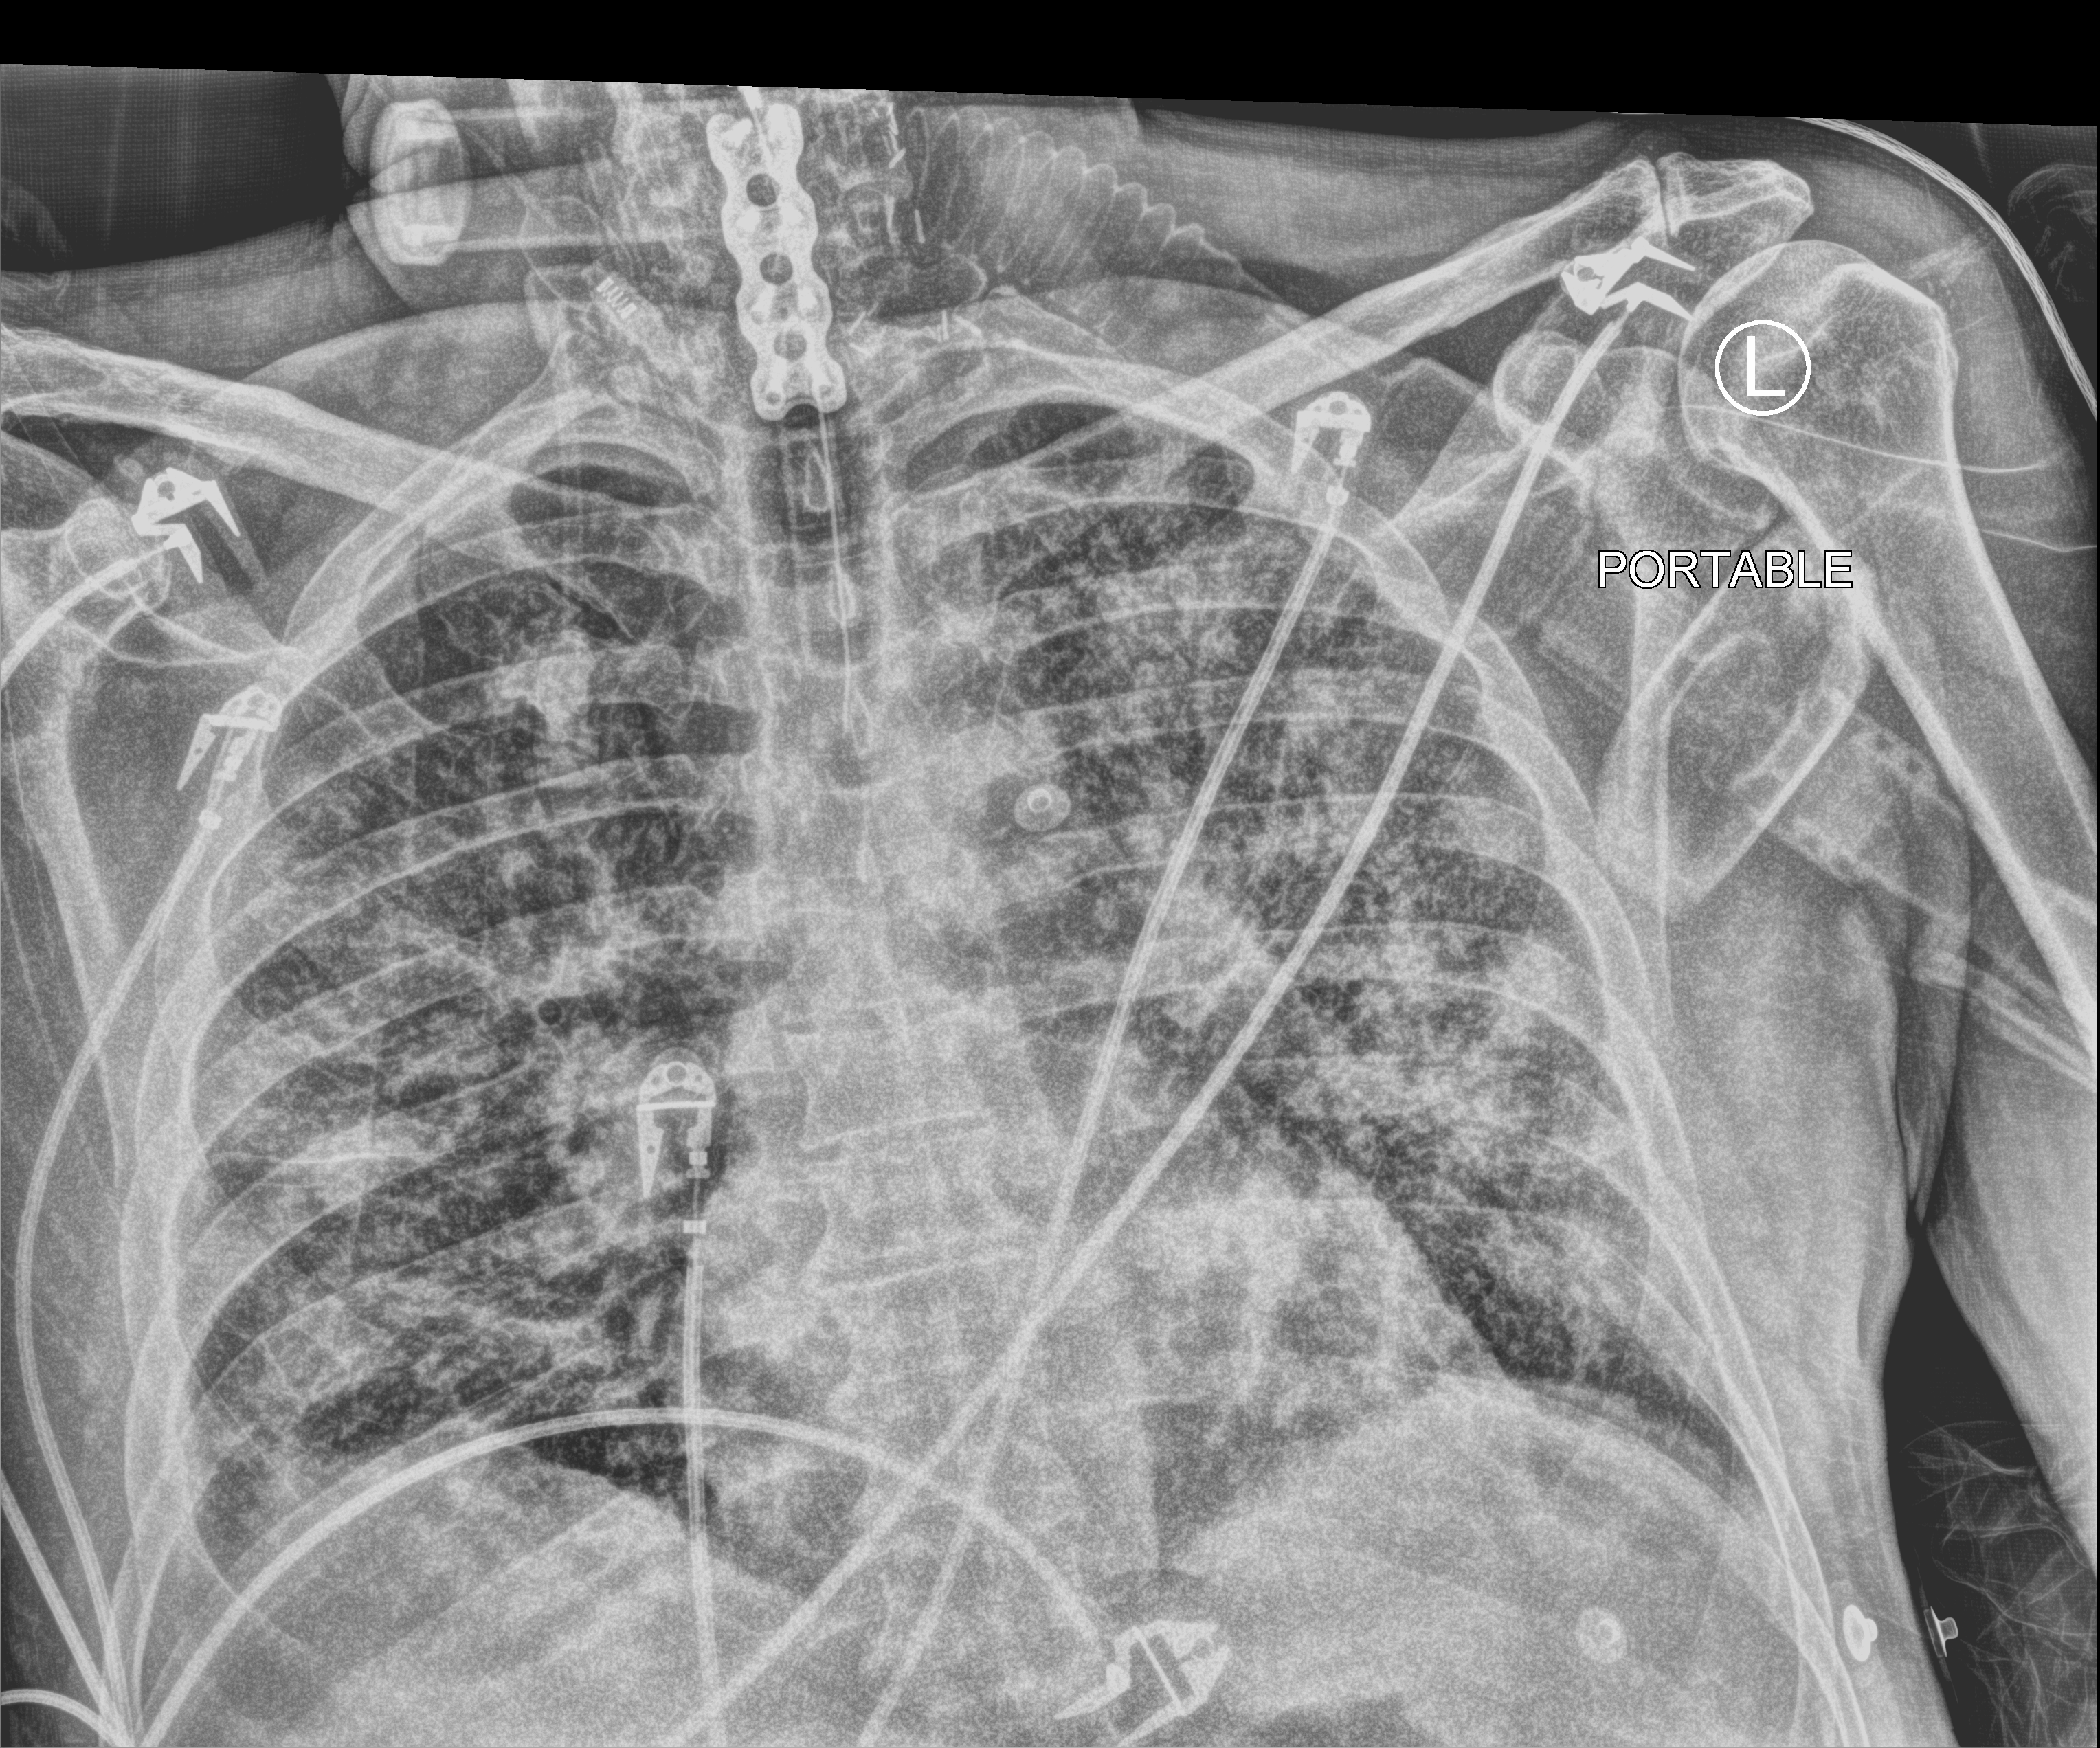
Portable chest radiograph, anteroposterior (AP) projection. Patient hospitalised with COVID-19; male, aged 60–74 years.
Hospital-stay facts (about this admission, not read from this image; timing relative to this image not recorded): admitted to intensive care during this hospital stay: yes.